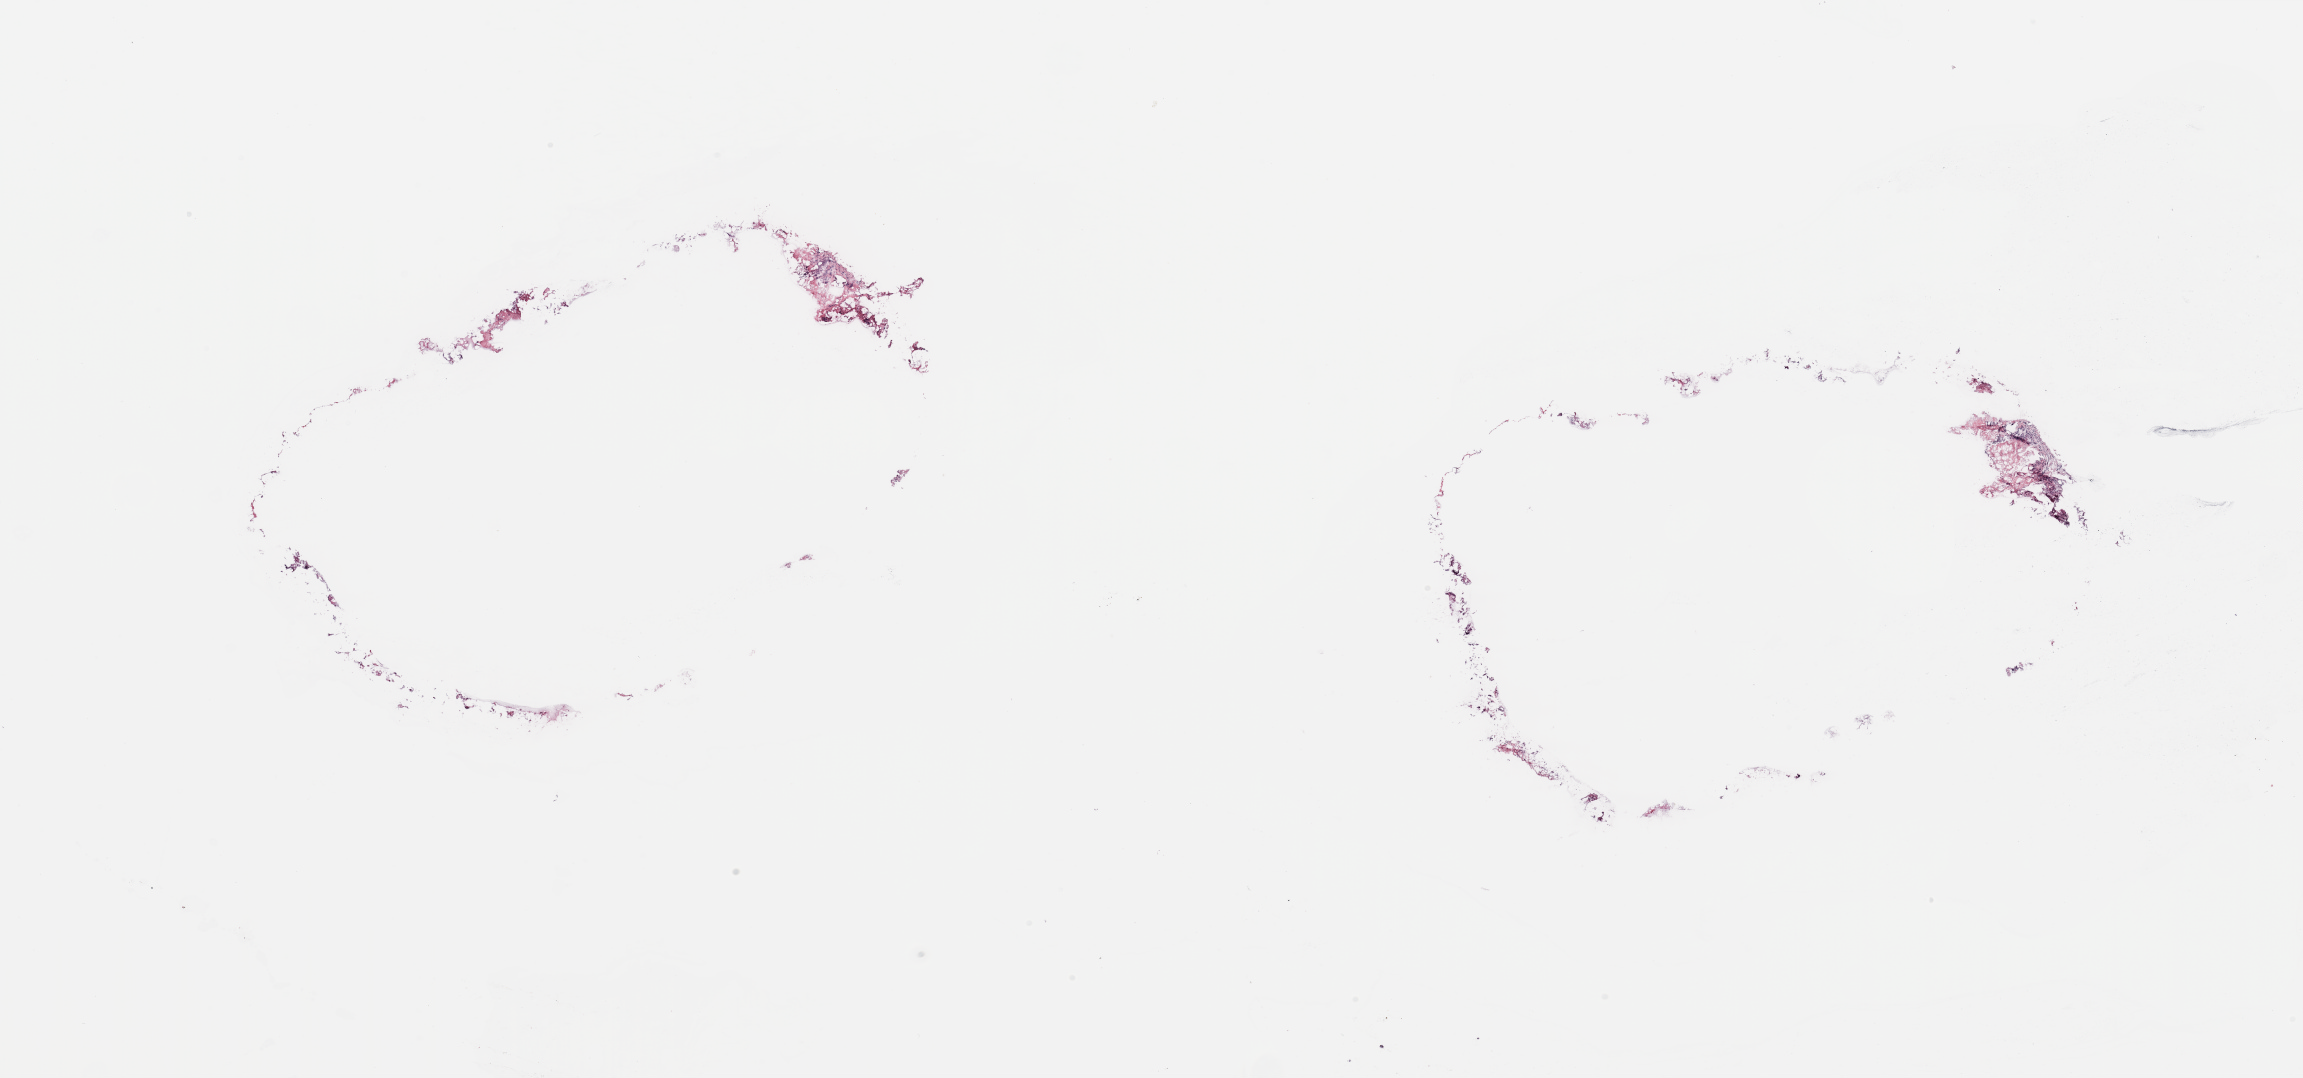
H&E-stained whole-slide image, whole scanned area (about 36.4 x 17.0 mm) shown as a low-resolution overview. Breast, tissue type not recorded.
Patient diagnosis (cohort enrolment): breast cancer (breast).